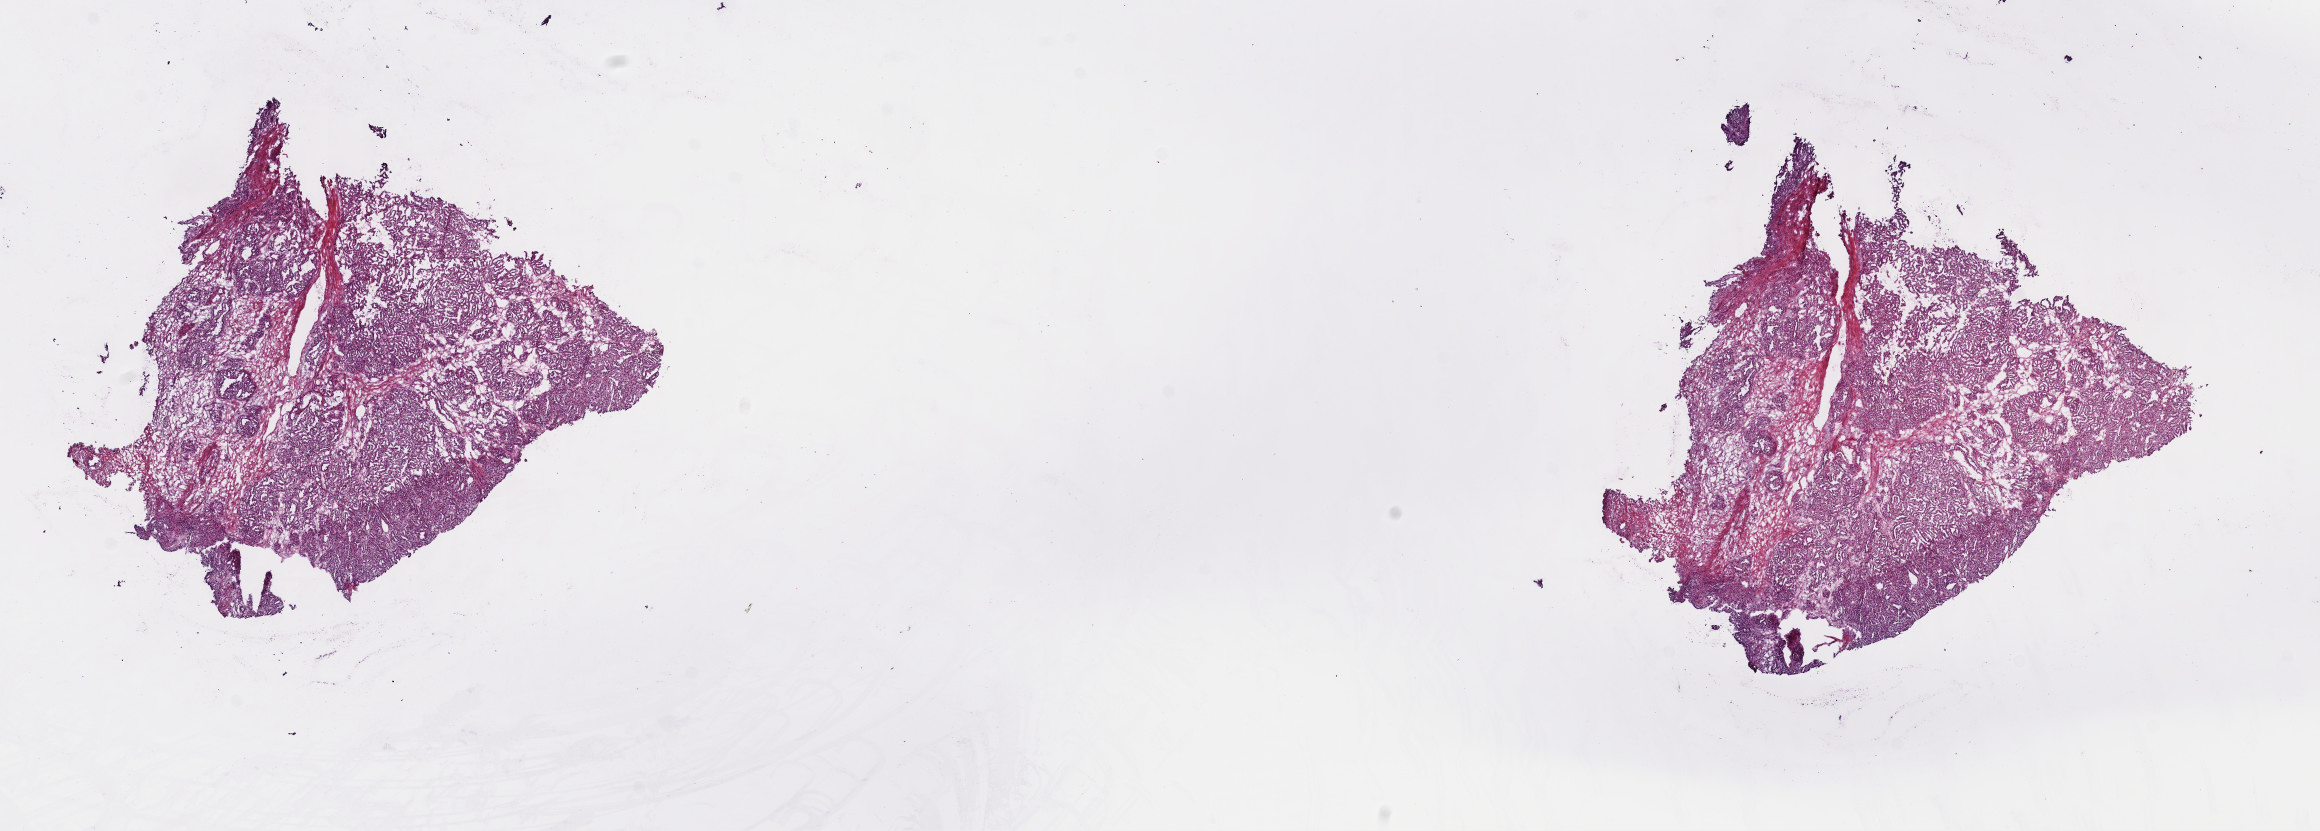
Whole-slide histology image, H&E, shown as a low-resolution overview of the whole scanned area (about 18.2 x 6.5 mm, slide scanned at 40x). Frozen section from the top of the tissue portion. Kidney, additional new primary tumour sample. Patient: male, age at initial diagnosis 55 years. Pathologist review of this section (percent, as recorded): tumour cells 85%, tumour nuclei 90%, normal cells 0%, stromal cells 15%, necrosis 0%. Inflammatory infiltration, as recorded: lymphocyte infiltration 0%, monocyte infiltration 0%, neutrophil infiltration 0%.
This section: additional new primary tumour. Patient diagnosis: Clear cell adenocarcinoma, NOS.